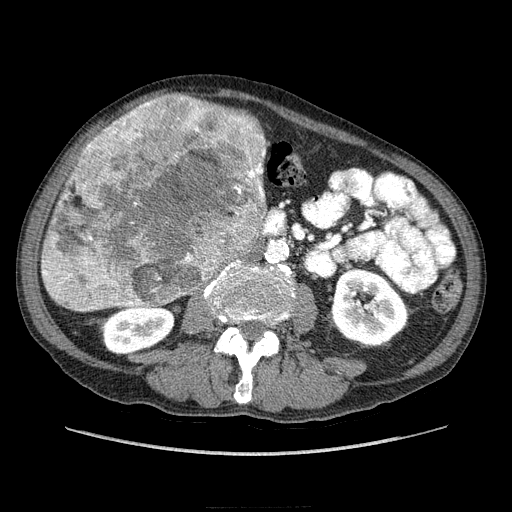
Contrast-enhanced abdominal CT (liver protocol), one axial slice. Position 75 of 218 along the scan axis. Reconstruction kernel STANDARD. 100 kVp. Soft-tissue window (W 400 / L 40 HU). 2.5 mm slice thickness. 512 × 512 image matrix, field of view 380 × 380 mm. From the clinical record (not read from this slice): diagnosis: hepatocellular carcinoma (patient treated with transarterial chemoembolisation; whether this scan precedes or follows treatment is not stated here); TNM stage (as recorded): Stage-IIIA; Child-Pugh class: A; tumour differentiation: well differentiated; tumour nodularity: multinodular.
Structures marked on this image (semi-automatic segmentation, software-assisted and operator-edited):
- liver parenchyma outside the tumour (the mass and vessels are separate outlines, so this box may not span the whole liver): bounding box (x1, y1, x2, y2) in pixels: (42, 128, 256, 312)
- mass: (42, 94, 269, 311)